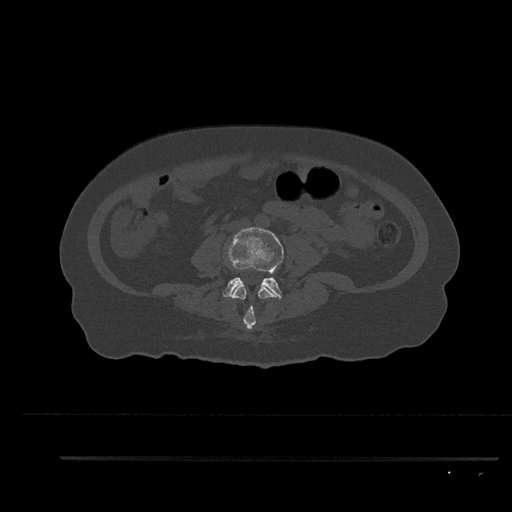
CT including the spine, one axial slice; position 47 of 797 along the scan axis; reconstruction kernel Br40s/3; bone window (W 1800 / L 400 HU); 0.5 mm slice thickness; 512 × 512 image matrix, field of view 408 × 408 mm. Female patient, age 44 years. From the clinical record (not read from this slice): primary cancer: renal.
Outlined on this slice (semi-automatic segmentation, software-assisted and operator-edited):
- L3 vertebra: bounding box [x1, y1, x2, y2] px = [231, 285, 282, 330]
- L4 vertebra: [223, 227, 284, 299]